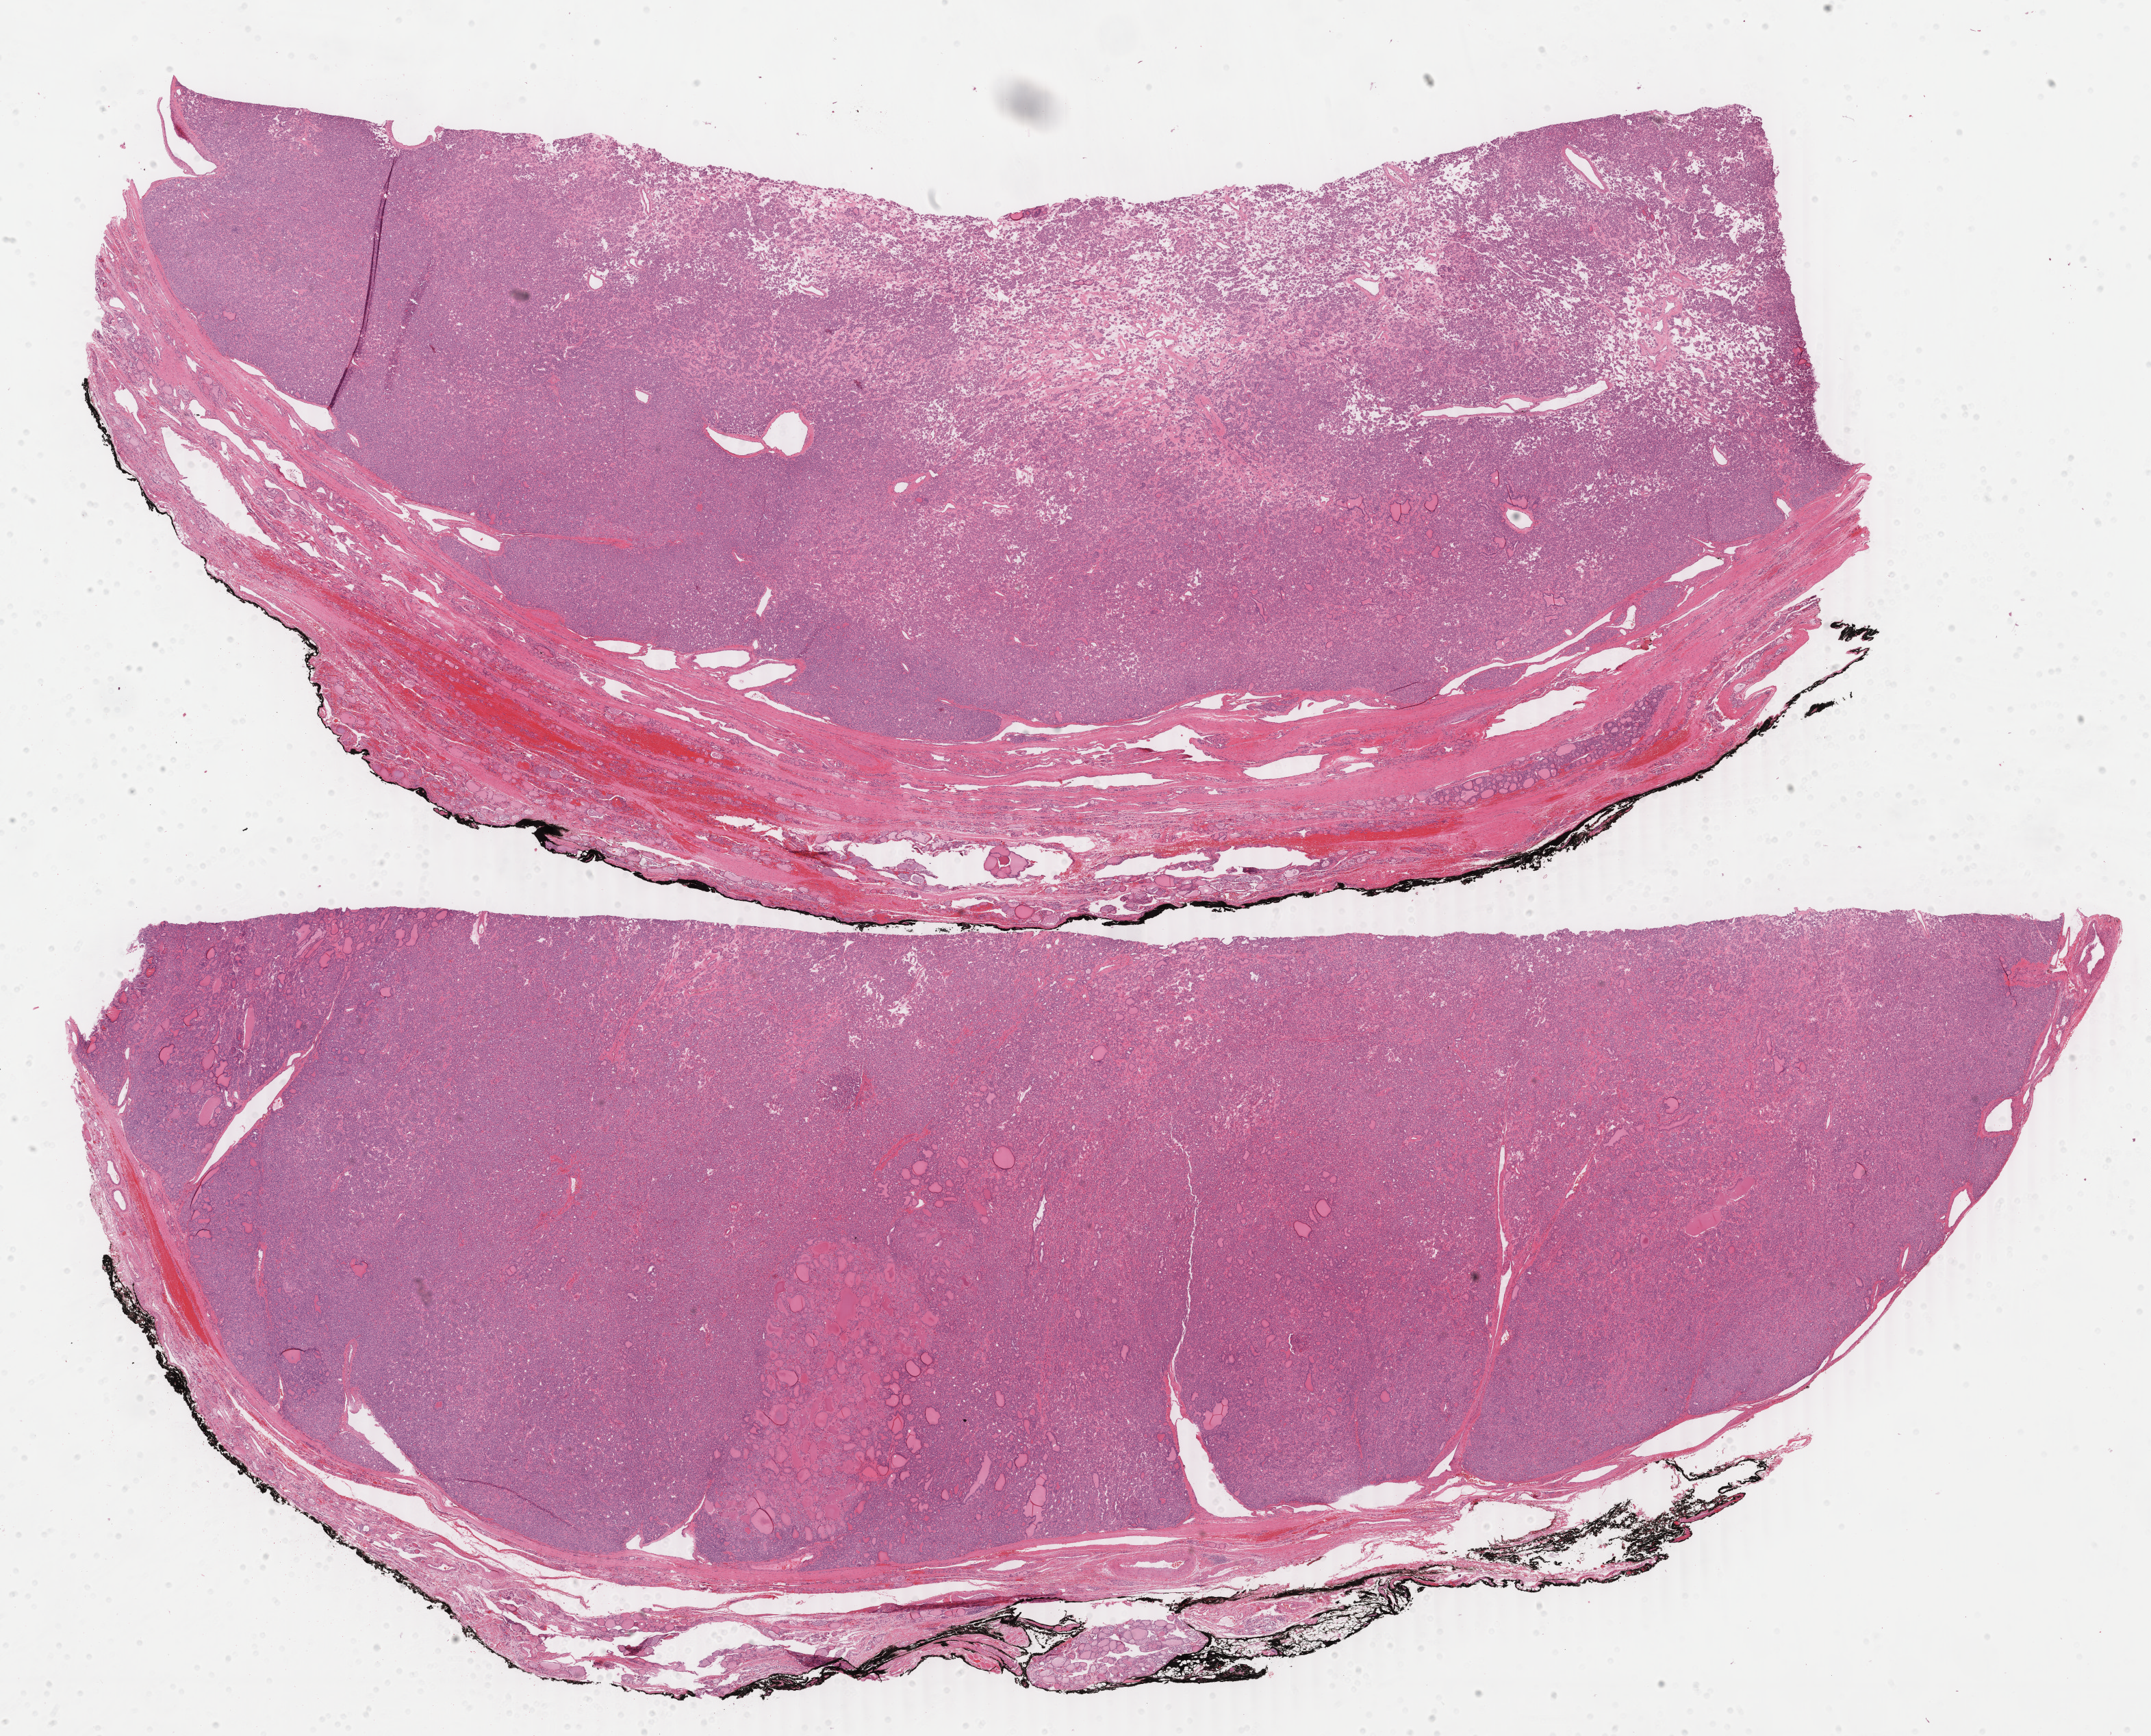
H&E whole-slide image, low-resolution overview of the scanned area, about 25.0 x 20.2 mm (from a 40x scan). Formalin-fixed paraffin-embedded (FFPE) diagnostic section. Thyroid, primary tumour sample. Female patient; age at initial diagnosis 80 years.
Diagnosis: Papillary adenocarcinoma, NOS (thyroid gland).